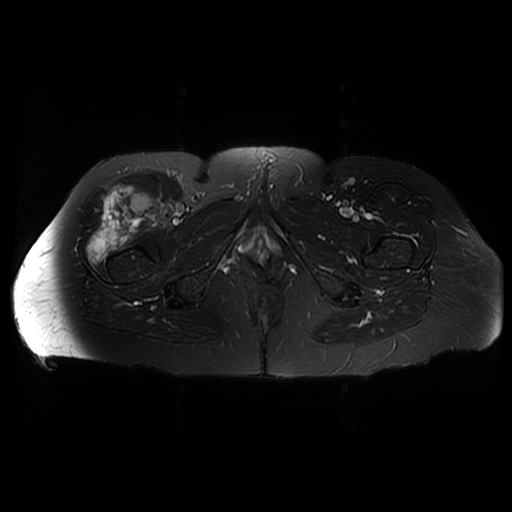
MRI of an extremity soft-tissue mass, one axial slice; slice 32 of 42 in the series (ordered by position); T2-weighted fat-saturated; 6 mm slice thickness; 512 × 512 image matrix, field of view 440 × 440 mm. Female patient. Case-level facts recorded for this patient, not image findings: histological type: pleiomorphic undifferentiated sarcoma; grade: high; site of the primary tumour: right quadricep.
Outlined on this slice (manually delineated by an expert):
- gross tumour volume including surrounding oedema: box from (x=87, y=183) to (x=162, y=264) px
- gross tumour volume (mass): (x=102, y=183)–(x=162, y=237)